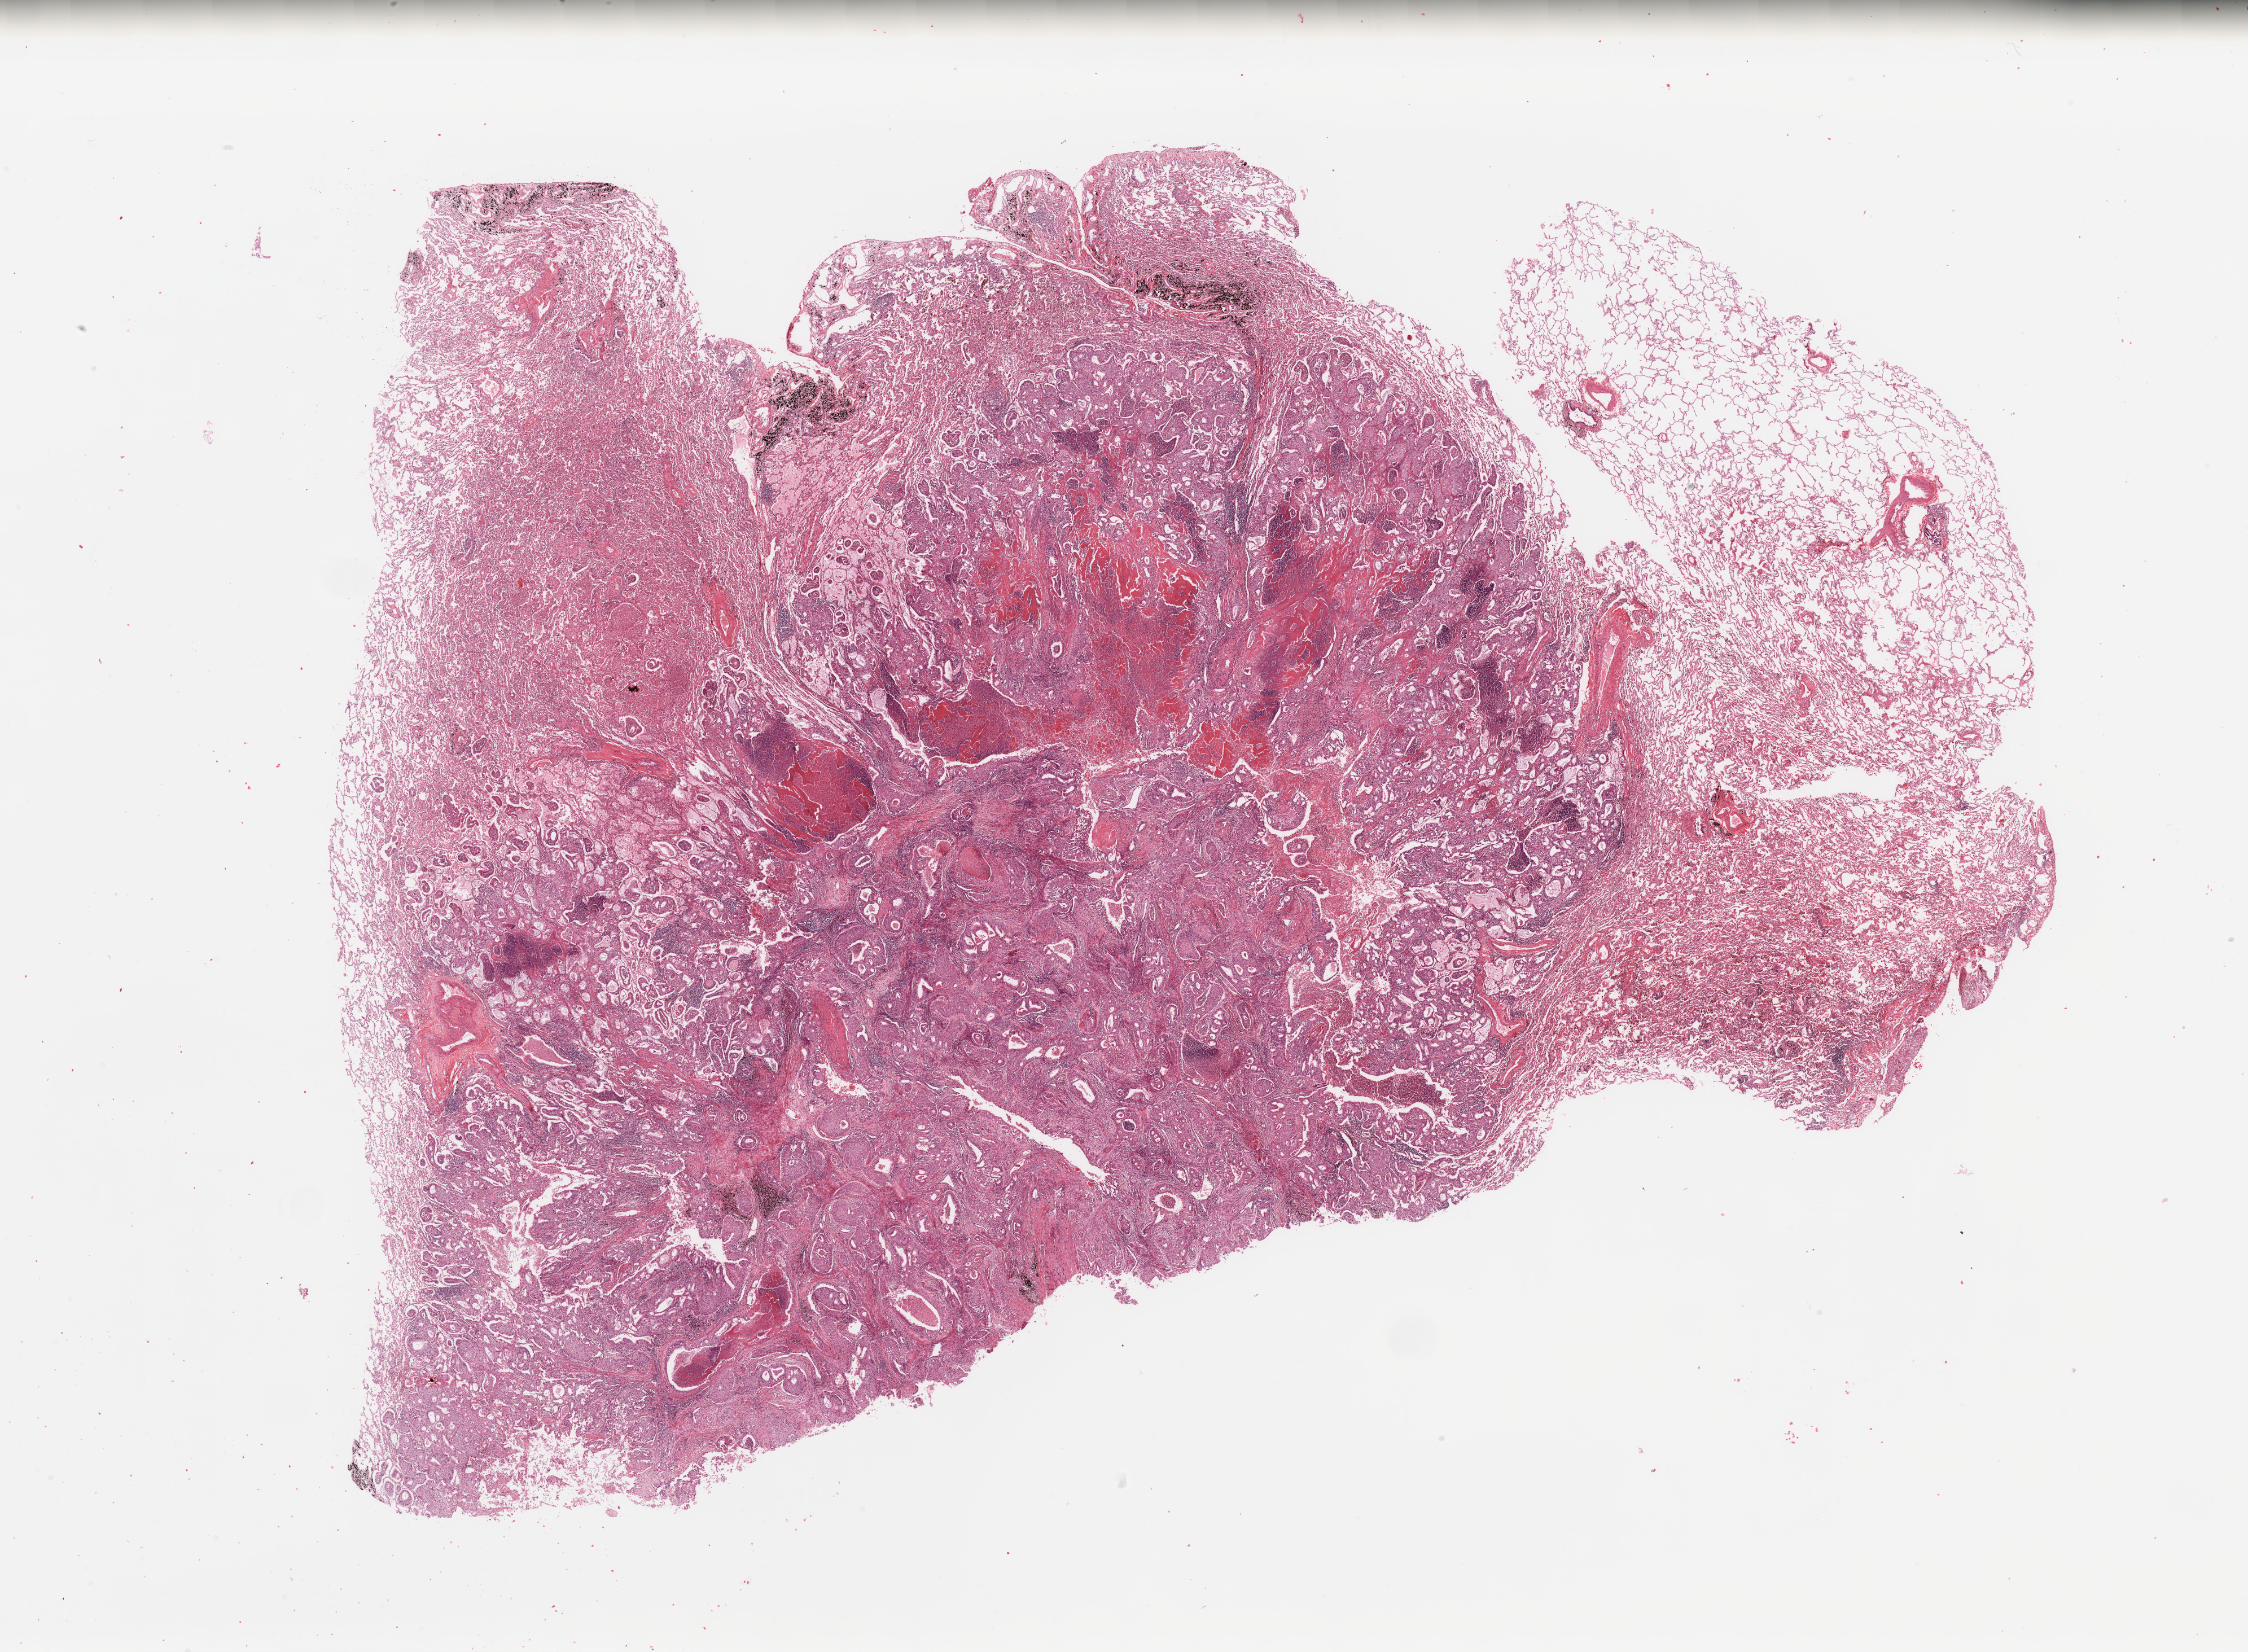
Digitized H&E tissue section (whole slide) — shown as a low-resolution overview of the whole scanned area (about 31.5 x 23.1 mm); lung, tumour tissue. Male, 61 y/o. Histologic grade: G3 (poorly differentiated).
* diagnosis: Adenocarcinoma, NOS
* AJCC pathologic stage: IB